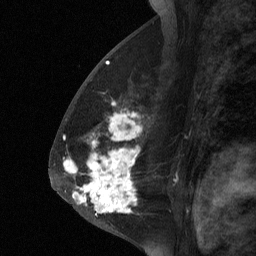
Breast MRI (dynamic contrast-enhanced), one sagittal slice. Position 37 of 64 along the scan axis. Dynamic contrast-enhanced study with each time point stored as its own series, time point 2 of 3 at this slice position (early post-contrast, ordered by acquisition time). 1.5 T. TE 4.8 ms, TR 27 ms. 2 mm slice thickness. 256 × 256 image matrix, field of view 180 × 180 mm. Female patient, age 56 years. Case-level facts recorded for this patient, not image findings: setting: breast cancer imaged before/during neoadjuvant chemotherapy; receptor status: HER2-positive.
Structures marked on this image (semi-automatic segmentation, software-assisted and operator-edited):
- analysis volume of interest (the breast-tissue region the enhancement analysis was run in; not a lesion): box from (x=59, y=105) to (x=149, y=229) px
- tumour enhancement mask (voxels above the 90 % enhancement threshold inside the analysis volume of interest): (x=64, y=154)–(x=135, y=213)